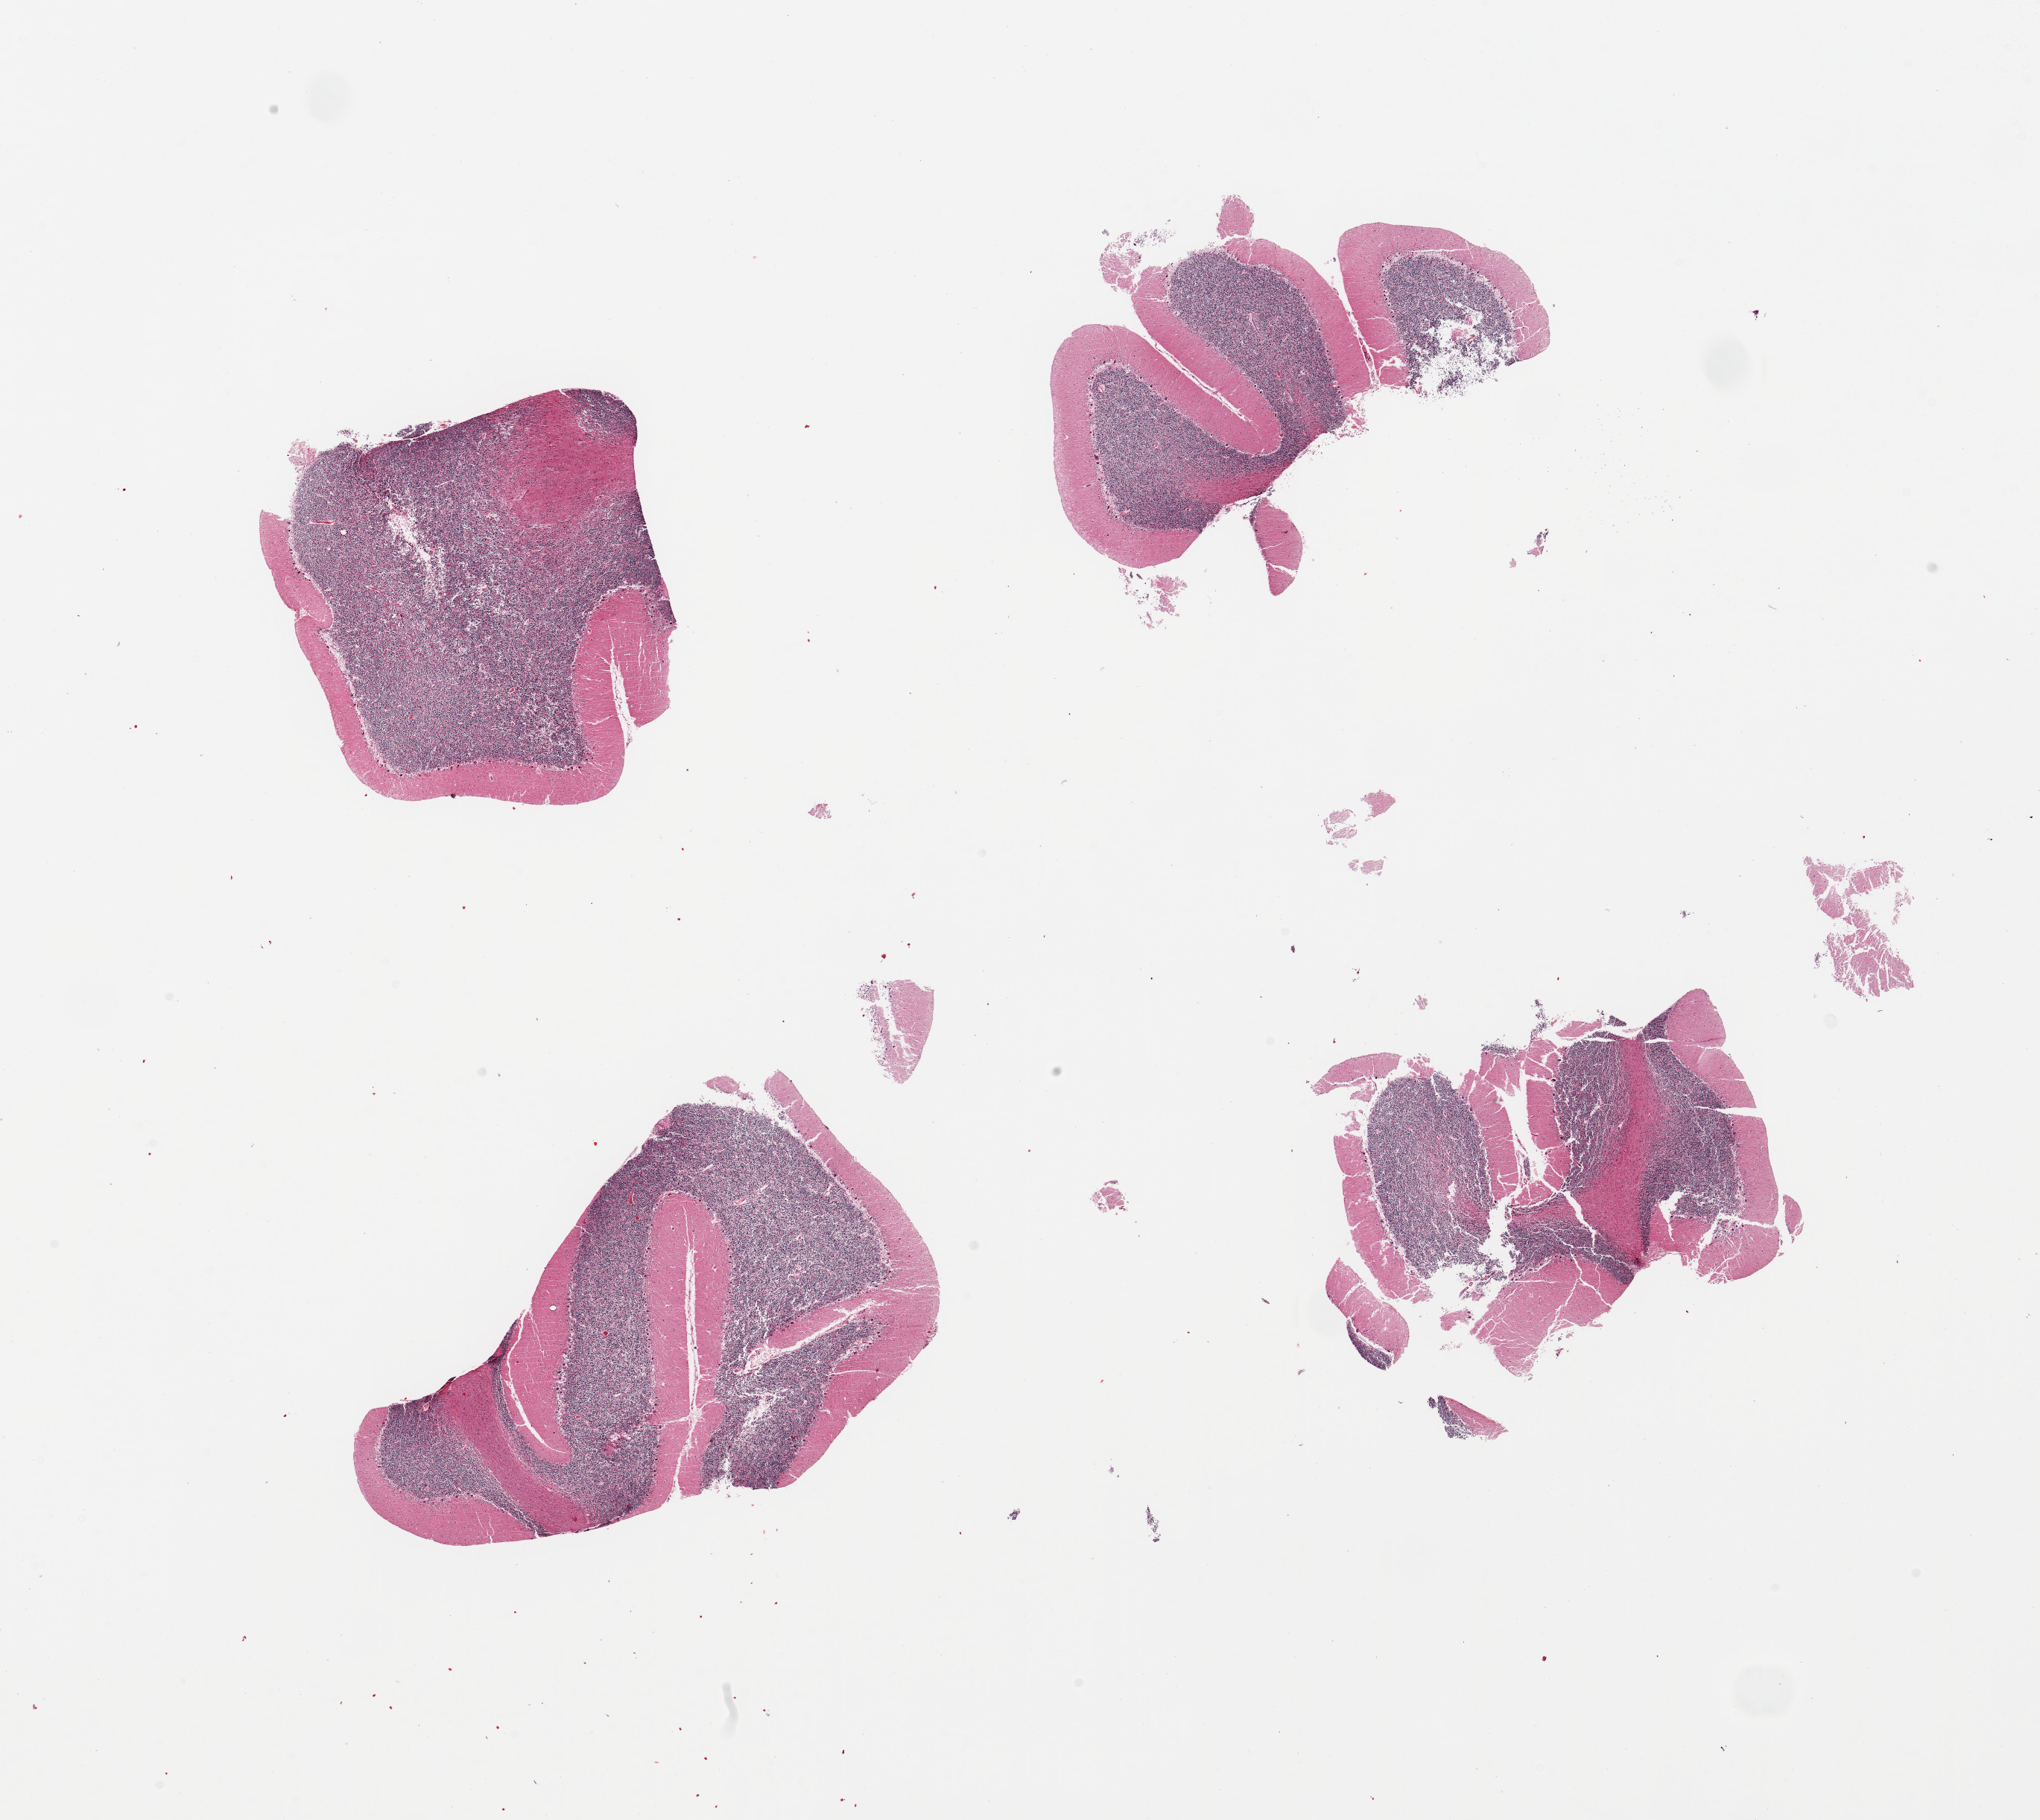
Haematoxylin and eosin whole-slide image, brightfield — shown as a low-resolution overview of the whole scanned area (about 21.7 x 19.3 mm); PAXgene-fixed, paraffin-embedded tissue; sampled site (target tissue): cerebellum; tissue donor sample. Male donor.
* reviewer comment on this tissue sample: 4 pieces, no abnormalities